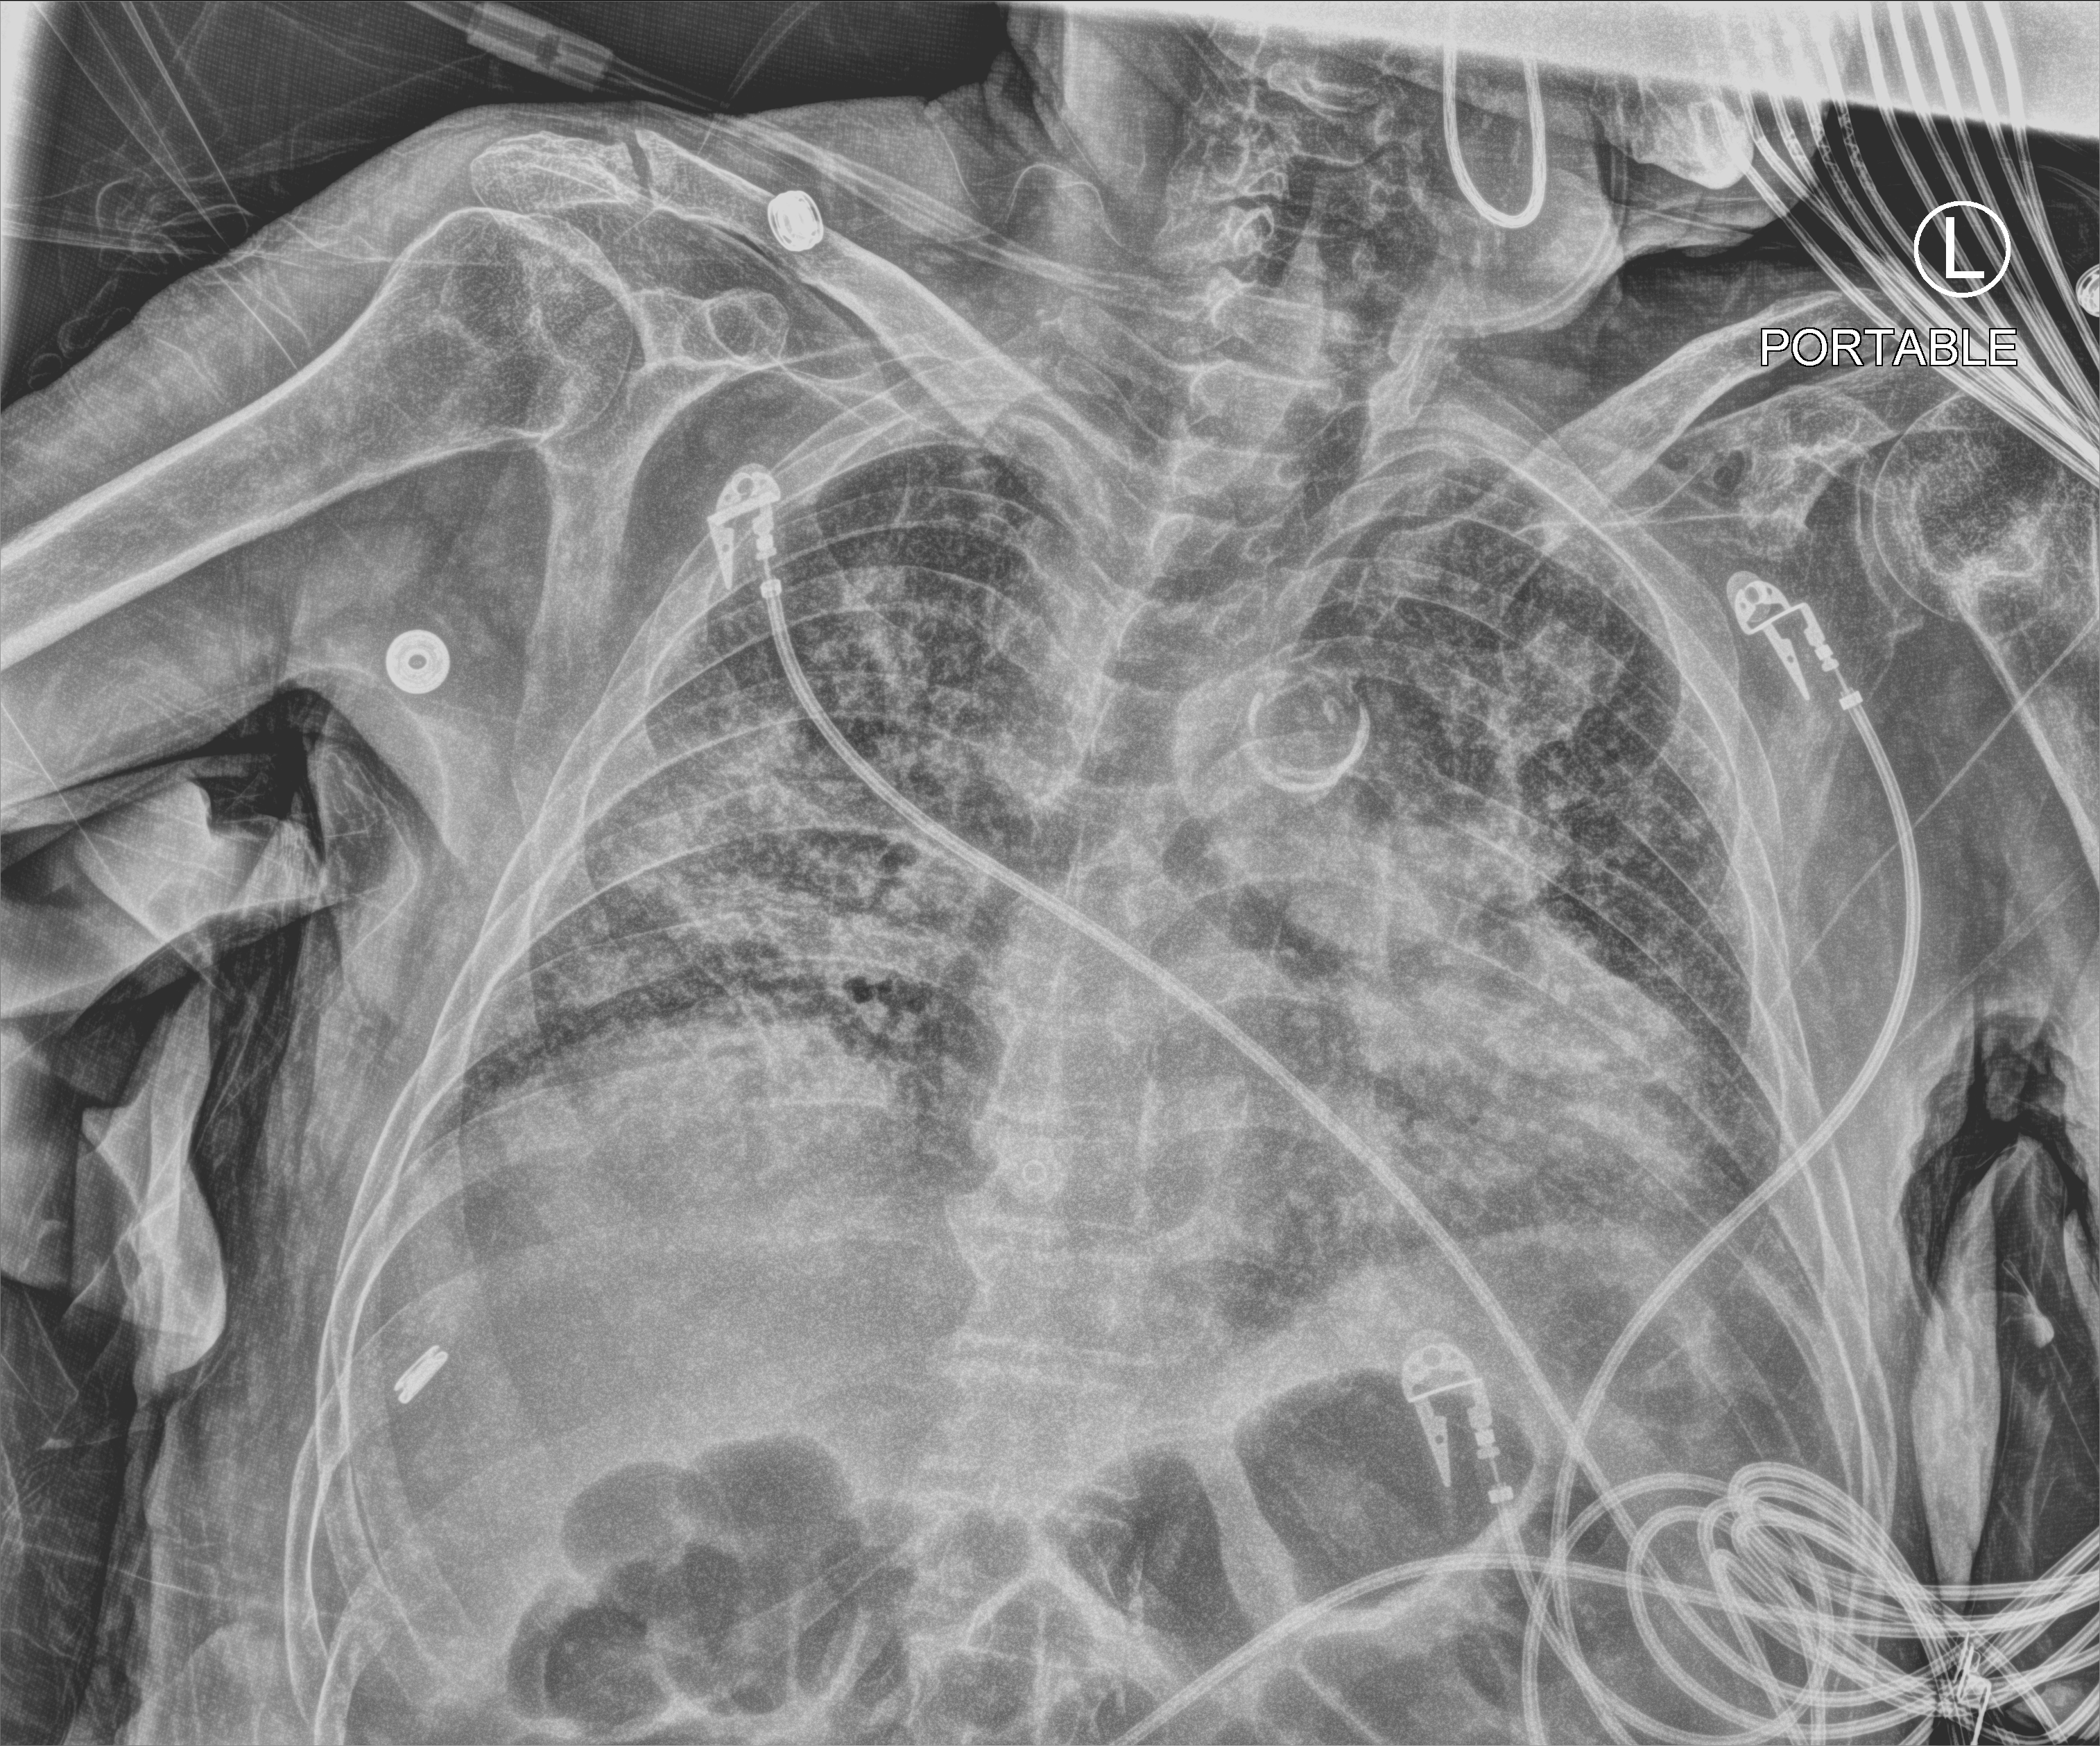
Portable chest radiograph. Patient hospitalised with COVID-19; male, aged 60–74 years.
Admission-level facts for this patient (not findings on this image; timing relative to this image not recorded):
- mechanically ventilated during this hospital stay: no
- COPD (admission record): no
- admitted to intensive care during this hospital stay: no